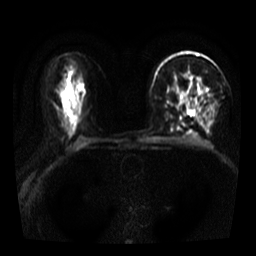
Breast MRI, one axial slice; slice 21 of 39 in the series (ordered by position); diffusion-weighted series; image 2 of 4 stored at this slice position (different b-values; order by instance number); 3 T; 5 mm slice thickness; 256 × 256 image matrix, field of view 320 × 320 mm. Female patient.
Outlined on this slice (manually delineated by an expert):
- tumour on diffusion-weighted imaging: bounding box <184,73,208,111> (left, top, right, bottom; pixels)